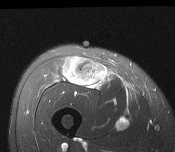
MRI of an extremity soft-tissue mass, one axial slice; slice 63 of 116 in the series (ordered by position); T2-weighted fat-saturated; MR volume resampled by the dataset authors to the PET/CT grid (not the native acquisition matrix); 3.27 mm slice thickness; 175 × 152 image matrix, field of view 171 × 148 mm. Male patient. Case-level facts recorded for this patient, not image findings: histological type: pleiomorphic leiomyosarcoma; grade: intermediate; site of the primary tumour: right thigh.
Structures marked on this image (expert contour drawn on MRI and transferred to this co-registered scan by the dataset authors):
- gross tumour volume including surrounding oedema: bounding box <61,58,109,87> (left, top, right, bottom; pixels)